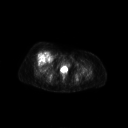
FDG PET of an extremity soft-tissue mass (from a PET/CT study), one axial slice; slice 62 of 267 in the series (ordered by position); 3.27 mm slice thickness; 128 × 128 image matrix, field of view 700 × 700 mm. Patient: female, 56 years. Case-level facts recorded for this patient, not image findings: histological type: malignant solitary fibrous tumor; grade: intermediate; site of the primary tumour: right thigh.
Annotated regions visible in this slice (expert contour drawn on MRI and transferred to this co-registered scan by the dataset authors):
- gross tumour volume including surrounding oedema: bounding box (x1, y1, x2, y2) in pixels: (36, 51, 50, 62)
- gross tumour volume (mass): (39, 52, 49, 59)